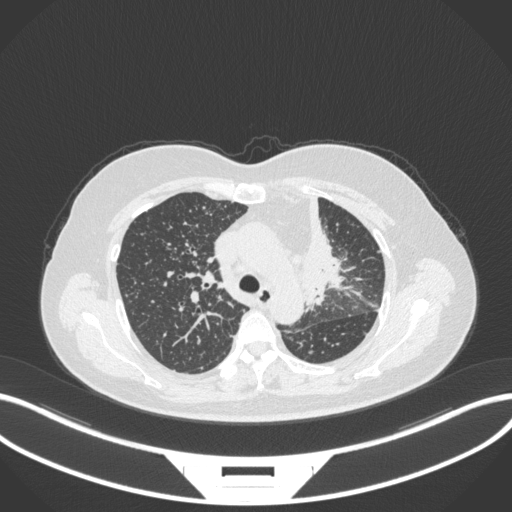
Chest CT, one axial slice. Position 234 of 348 along the scan axis. Reconstruction kernel B31f. Lung window (W 1500 / L -600 HU). 1 mm slice thickness. 512 × 512 image matrix, field of view 400 × 400 mm. Female patient, age 49 years. Case-level facts recorded for this patient, not image findings: clinical TNM (as recorded): T1c N0 M1.
Structures marked on this image (rectangle marked by the reading radiologist):
- lung tumour (recorded histology: adenocarcinoma): bounding box [x1, y1, x2, y2] px = [292, 192, 350, 310]